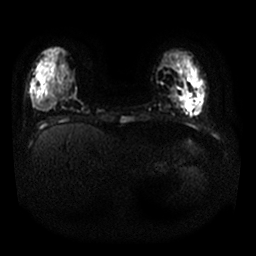
Breast MRI, one axial slice. Position 3 of 25 along the scan axis. Diffusion-weighted series; image 2 of 4 stored at this slice position (different b-values; order by instance number). 1.5 T. 4 mm slice thickness. 256 × 256 image matrix. Female patient.
Annotated regions visible in this slice (manually delineated by an expert):
- tumour on diffusion-weighted imaging: bounding box (x1, y1, x2, y2) in pixels: (185, 94, 193, 109)